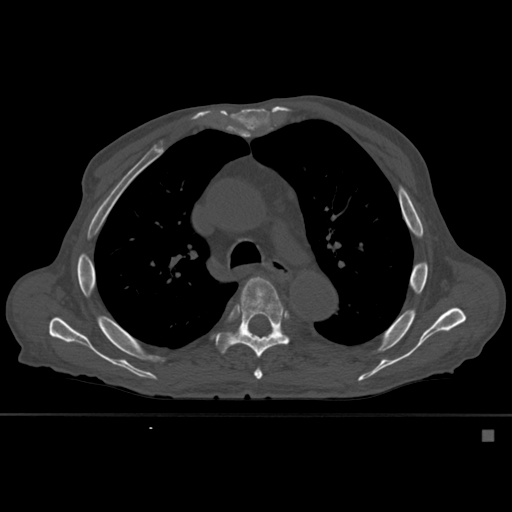
CT including the spine, one axial slice; position 387 of 527 along the scan axis; bone window (W 1800 / L 400 HU); 1.5 mm slice thickness; 512 × 512 image matrix, field of view 373 × 373 mm. Patient: male, 78 years. Case-level facts recorded for this patient, not image findings: primary cancer: prostate.
Structures marked on this image (semi-automatic segmentation, software-assisted and operator-edited):
- T5 vertebra: bounding box <246,345,263,380> (left, top, right, bottom; pixels)
- T6 vertebra: <216,277,289,358>